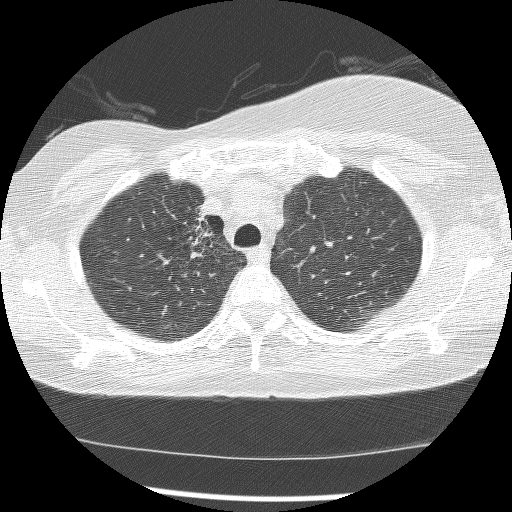
Low-dose screening chest CT, axial slice; first (baseline) screen; lung window (W 1500 / L -600 HU); 2.5 mm slice thickness; lung (sharp) reconstruction kernel (BONE); slice 35 of 172 in the series; 512 × 512 image matrix. Female participant, aged 56 years at enrolment.
Lesion marked by an expert reader, box from (x=165, y=202) to (x=223, y=275) px. The screening reader recorded 2 non-calcified nodules or masses ≥4 mm on this exam (right lower lobe, right middle lobe); which of them this box marks is not recorded. Official screen result: positive, change unspecified: nodule(s) >= 4 mm or enlarging nodule(s), mass(es), or other non-specific abnormalities suspicious for lung cancer. Participant outcome: lung cancer diagnosed 1185 days after this screen — adenocarcinoma, NOS, right upper lobe, stage IIIB (AJCC 6th edition), 8 mm at pathology.